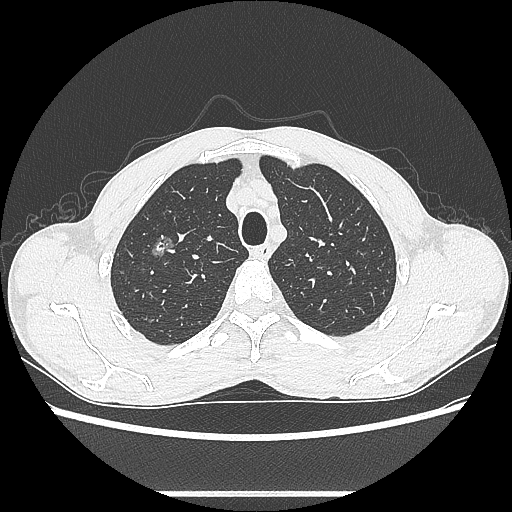
Chest CT, one axial slice; position 483 of 601 along the scan axis; 100 kVp; lung window (W 1500 / L -600 HU); 0.62 mm slice thickness; 512 × 512 image matrix, field of view 357 × 357 mm. Male patient, age 54 years. From the clinical record (not read from this slice): clinical TNM (as recorded): T1a N0 M0.
Structures marked on this image (rectangle marked by the reading radiologist):
- lung tumour (recorded histology: adenocarcinoma): bounding box [x1, y1, x2, y2] px = [150, 234, 183, 266]